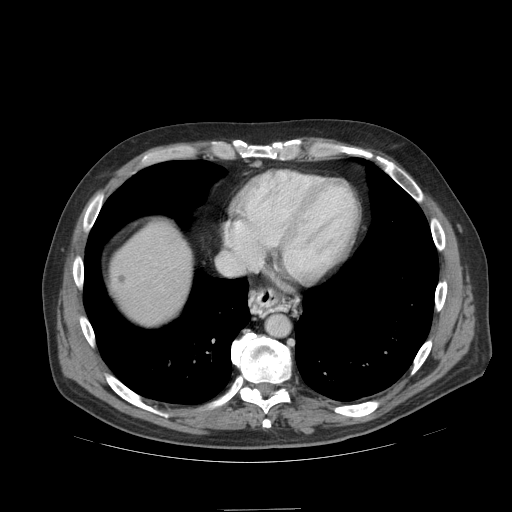
Contrast-enhanced abdominal CT (liver protocol), one axial slice; slice 93 of 99 in the series (ordered by position); soft-tissue window (W 400 / L 40 HU); 512 × 512 image matrix, field of view 440 × 440 mm. From the clinical record (not read from this slice): diagnosis: hepatocellular carcinoma (patient treated with transarterial chemoembolisation; whether this scan precedes or follows treatment is not stated here); TNM stage (as recorded): Stage-I; Child-Pugh class: A; tumour differentiation: no biopsy; tumour nodularity: uninodular.
Structures marked on this image (semi-automatic segmentation, software-assisted and operator-edited):
- abdominal aorta: bounding box [x1, y1, x2, y2] px = [266, 314, 289, 336]
- liver parenchyma outside the tumour (the mass and vessels are separate outlines, so this box may not span the whole liver): [110, 224, 192, 324]